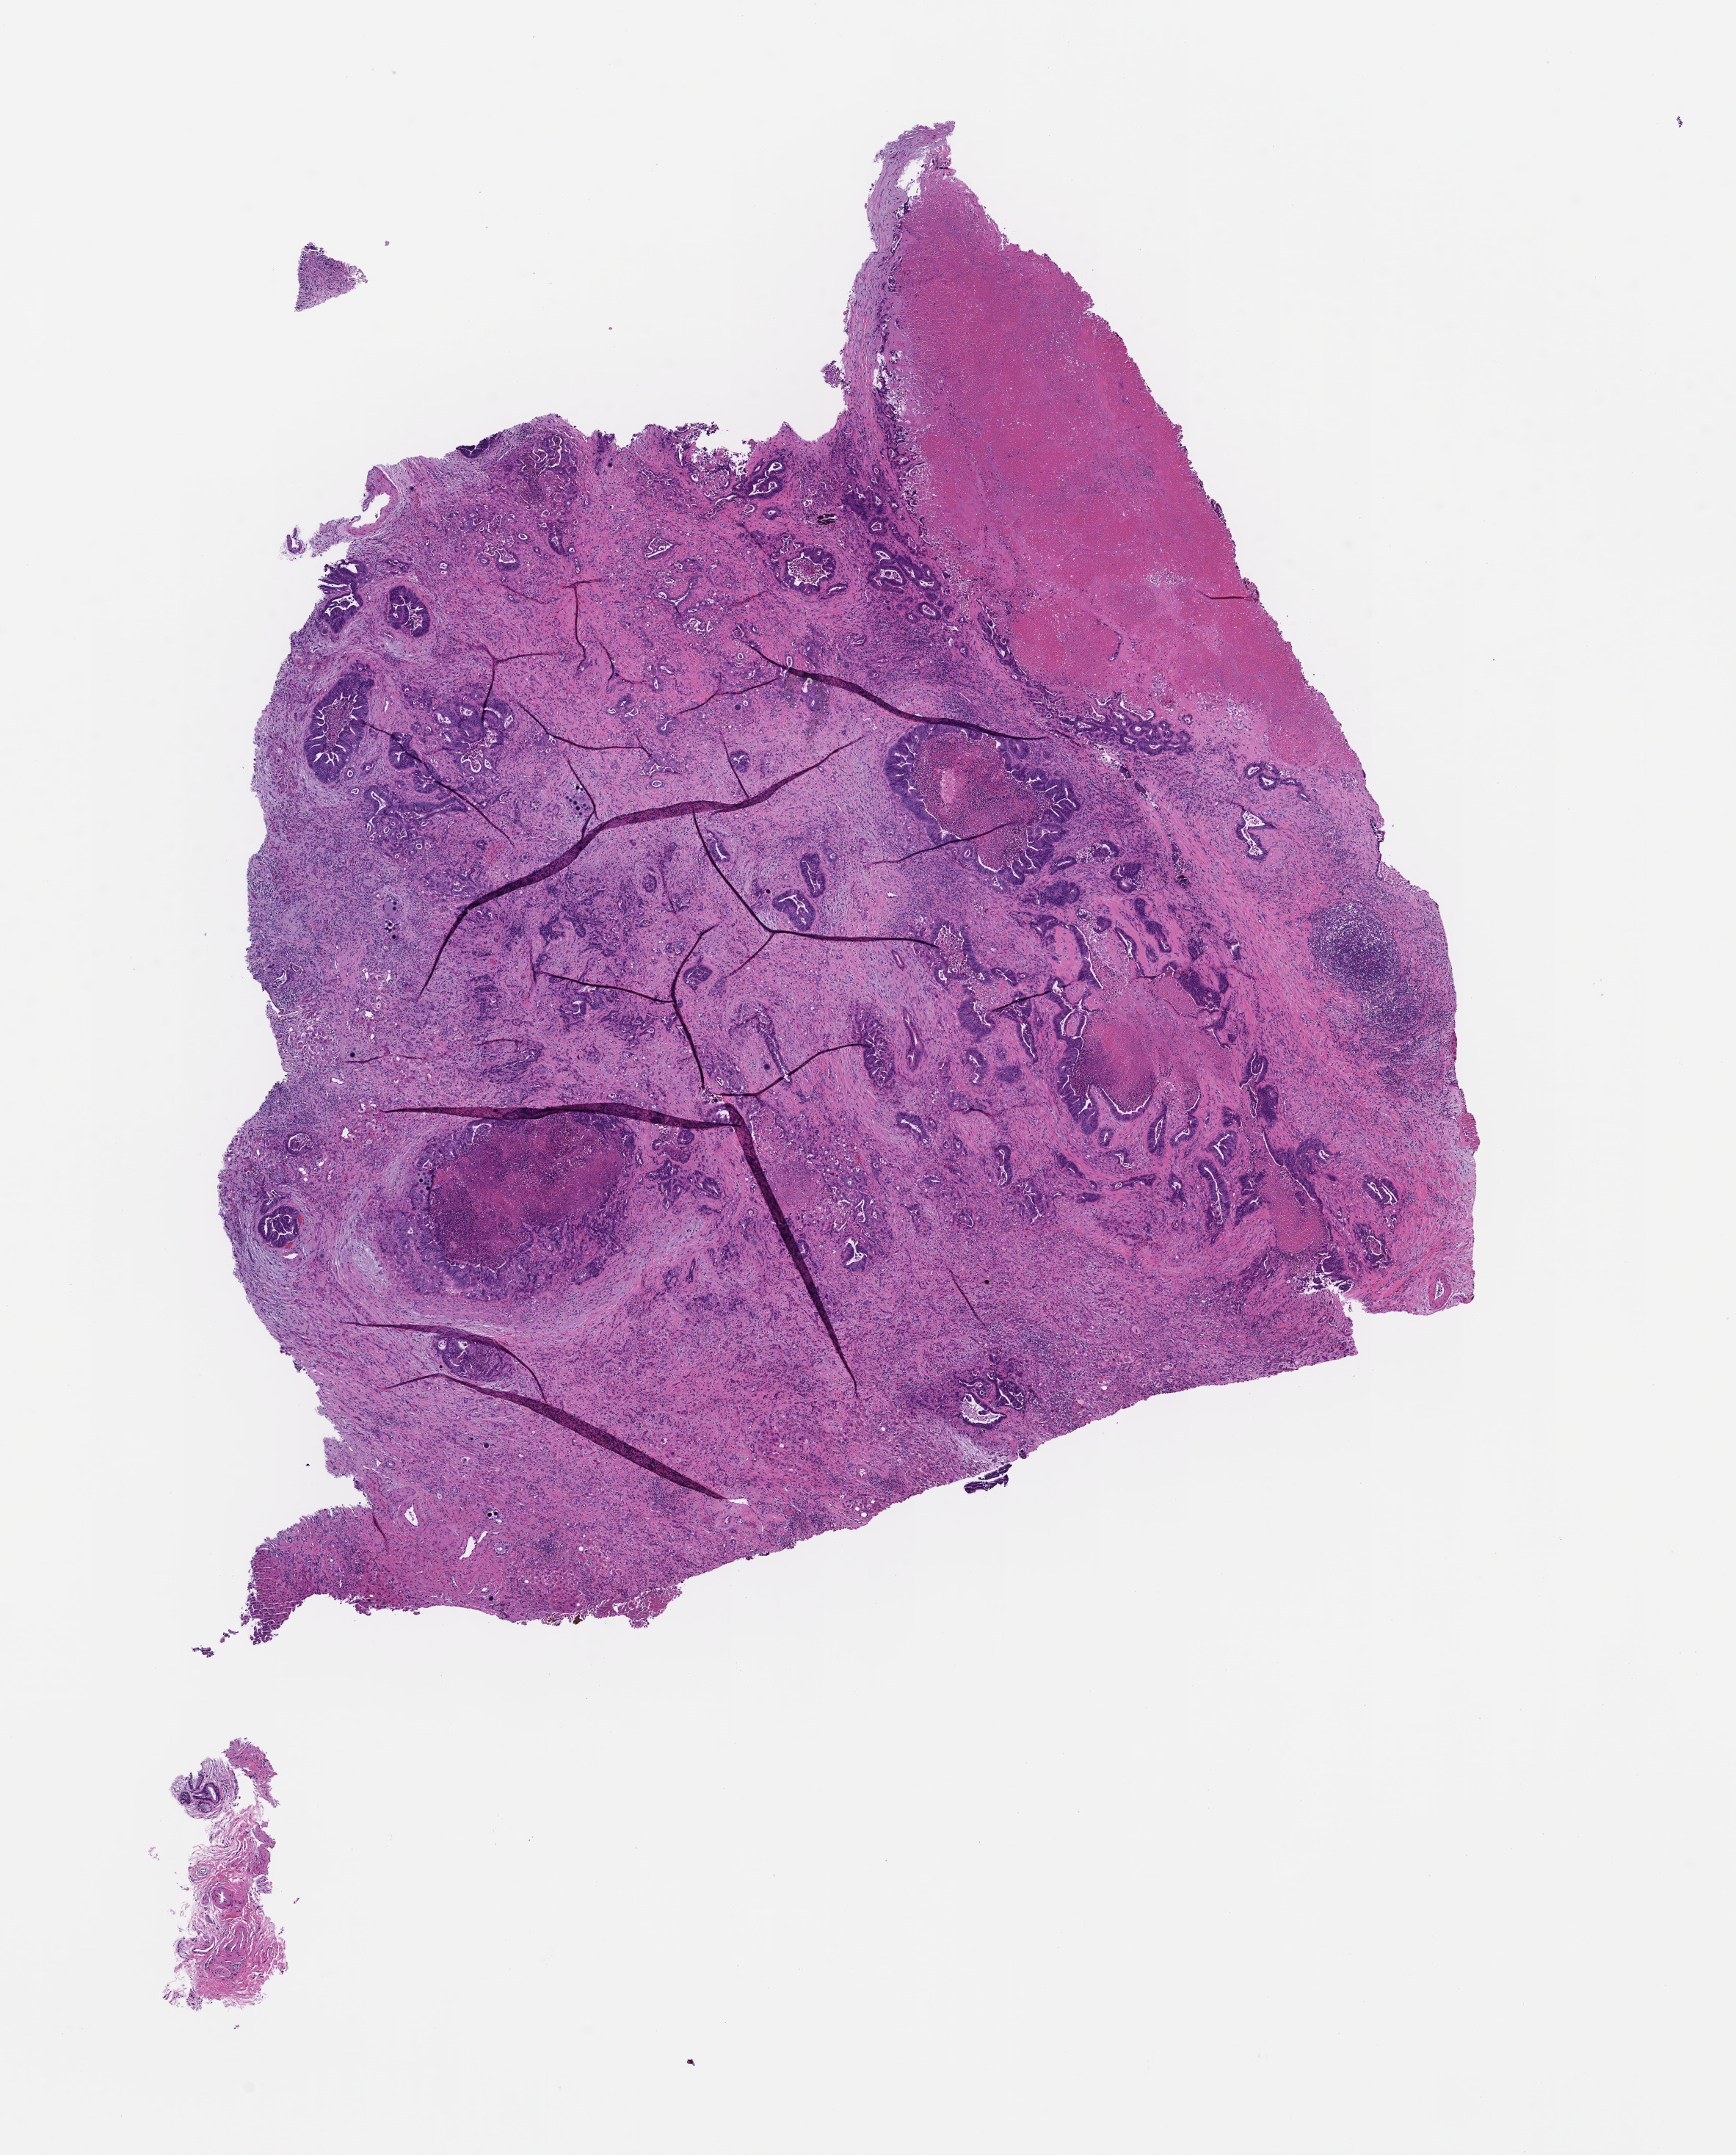
Digitized H&E-stained section, a low-resolution overview of the entire scanned area, about 9.5 x 11.9 mm. Formalin-fixed, paraffin-embedded (FFPE) tissue. Female patient.
* this section: metastatic tumor tissue
* patient diagnosis (primary): Colorectal Carcinoma